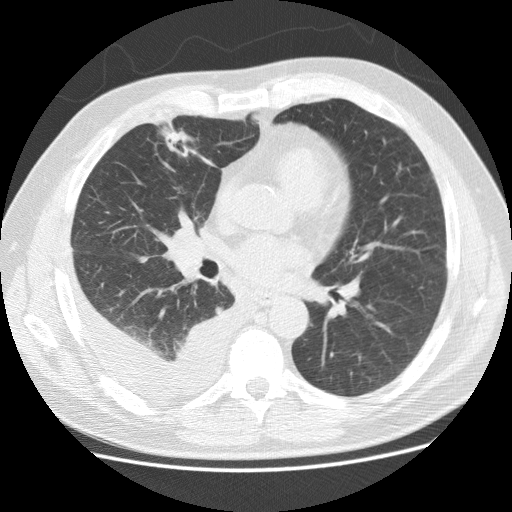
Low-dose screening chest CT, one axial slice. Slice 64 of 142 in the series (ordered by position). Reconstruction kernel STANDARD. 120 kVp. Lung window (W 1500 / L -600 HU). 2.5 mm slice thickness. 512 × 512 image matrix.
Structures marked on this image (outlined manually by an expert reader):
- lesion 1 (tumor, middle lobe of right lung): bounding box [x1, y1, x2, y2] px = [163, 129, 193, 157]